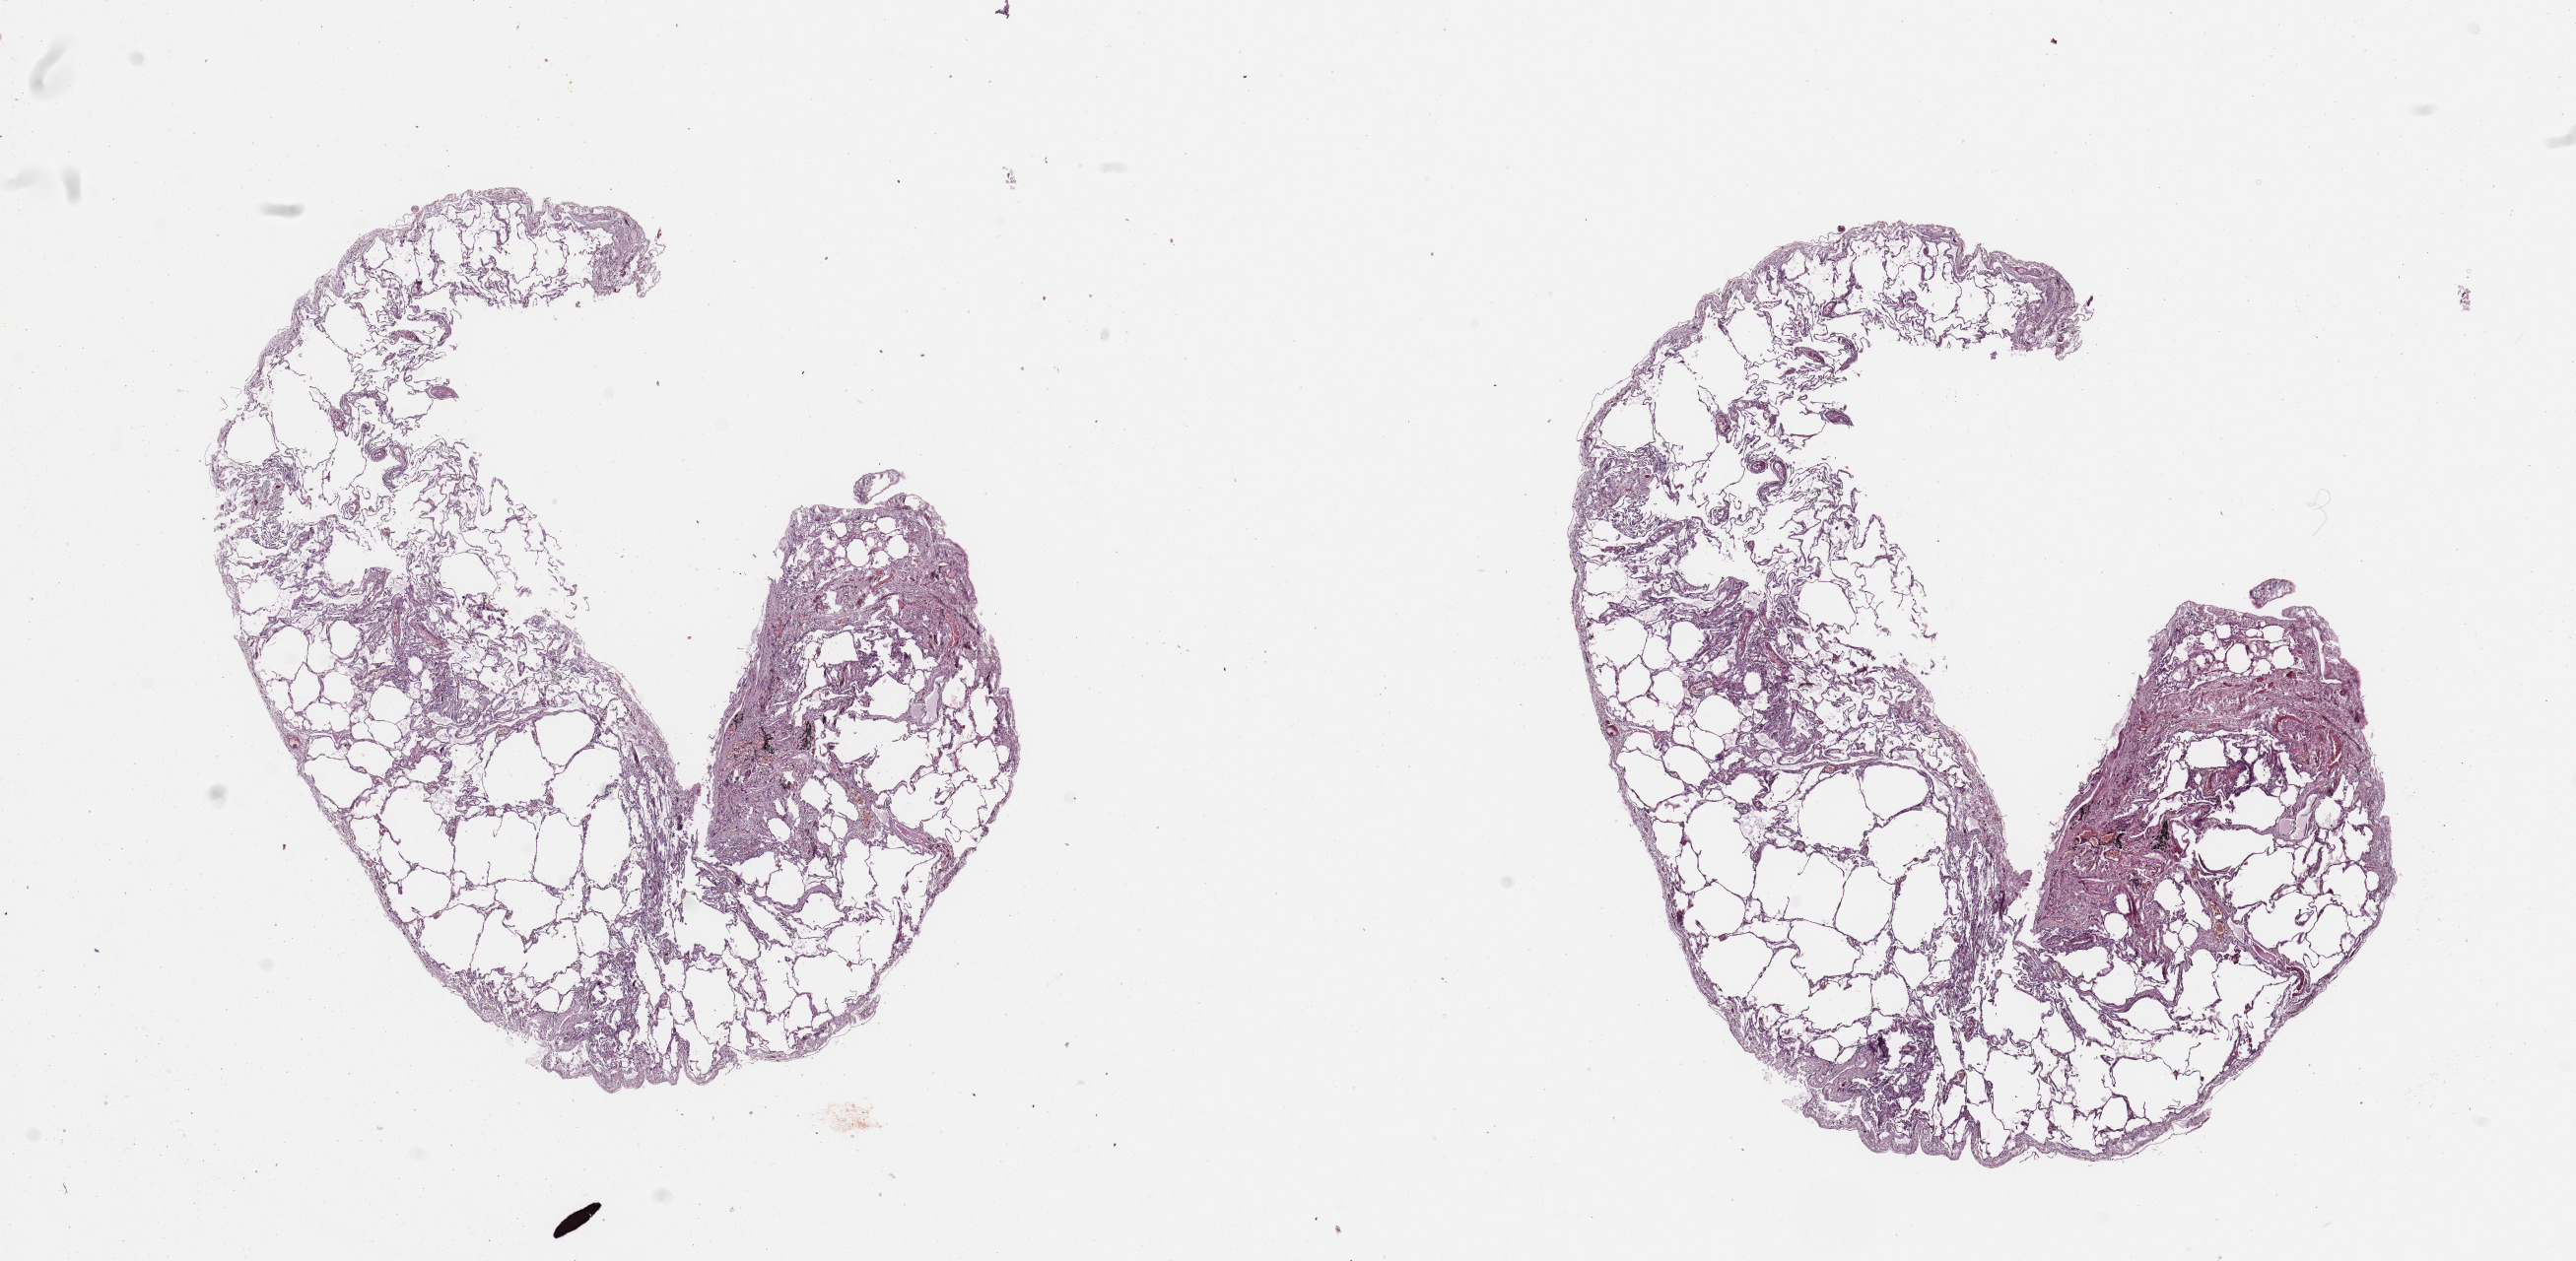
Hematoxylin and eosin (H&E) stained whole-slide image — a low-resolution overview of the entire scanned area, about 20.7 x 10.1 mm (acquisition: 20x scan); normal (non-tumour) tissue sample, sampled site: lung. Patient: male, age 76 years.
* this section: normal (non-tumour) tissue from the same patient
* patient diagnosis: Squamous cell carcinoma, NOS